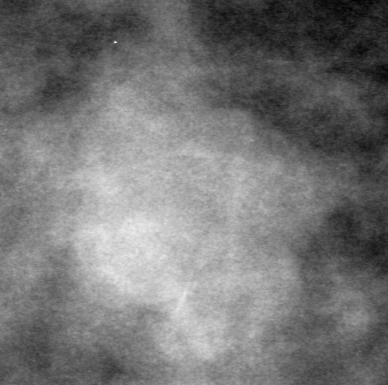
Cropped region of a digitized screen-film mammogram centred on a radiologist-marked abnormality; right breast; CC view; BI-RADS breast density category 3 (scale 1–4).
- Mass, shape lobulated, margins circumscribed; BI-RADS assessment category 0 (incomplete: needs additional imaging); subtlety rating 4 on a 1 (subtle) to 5 (obvious) scale; pathology result (as recorded, not read from the image): malignant.